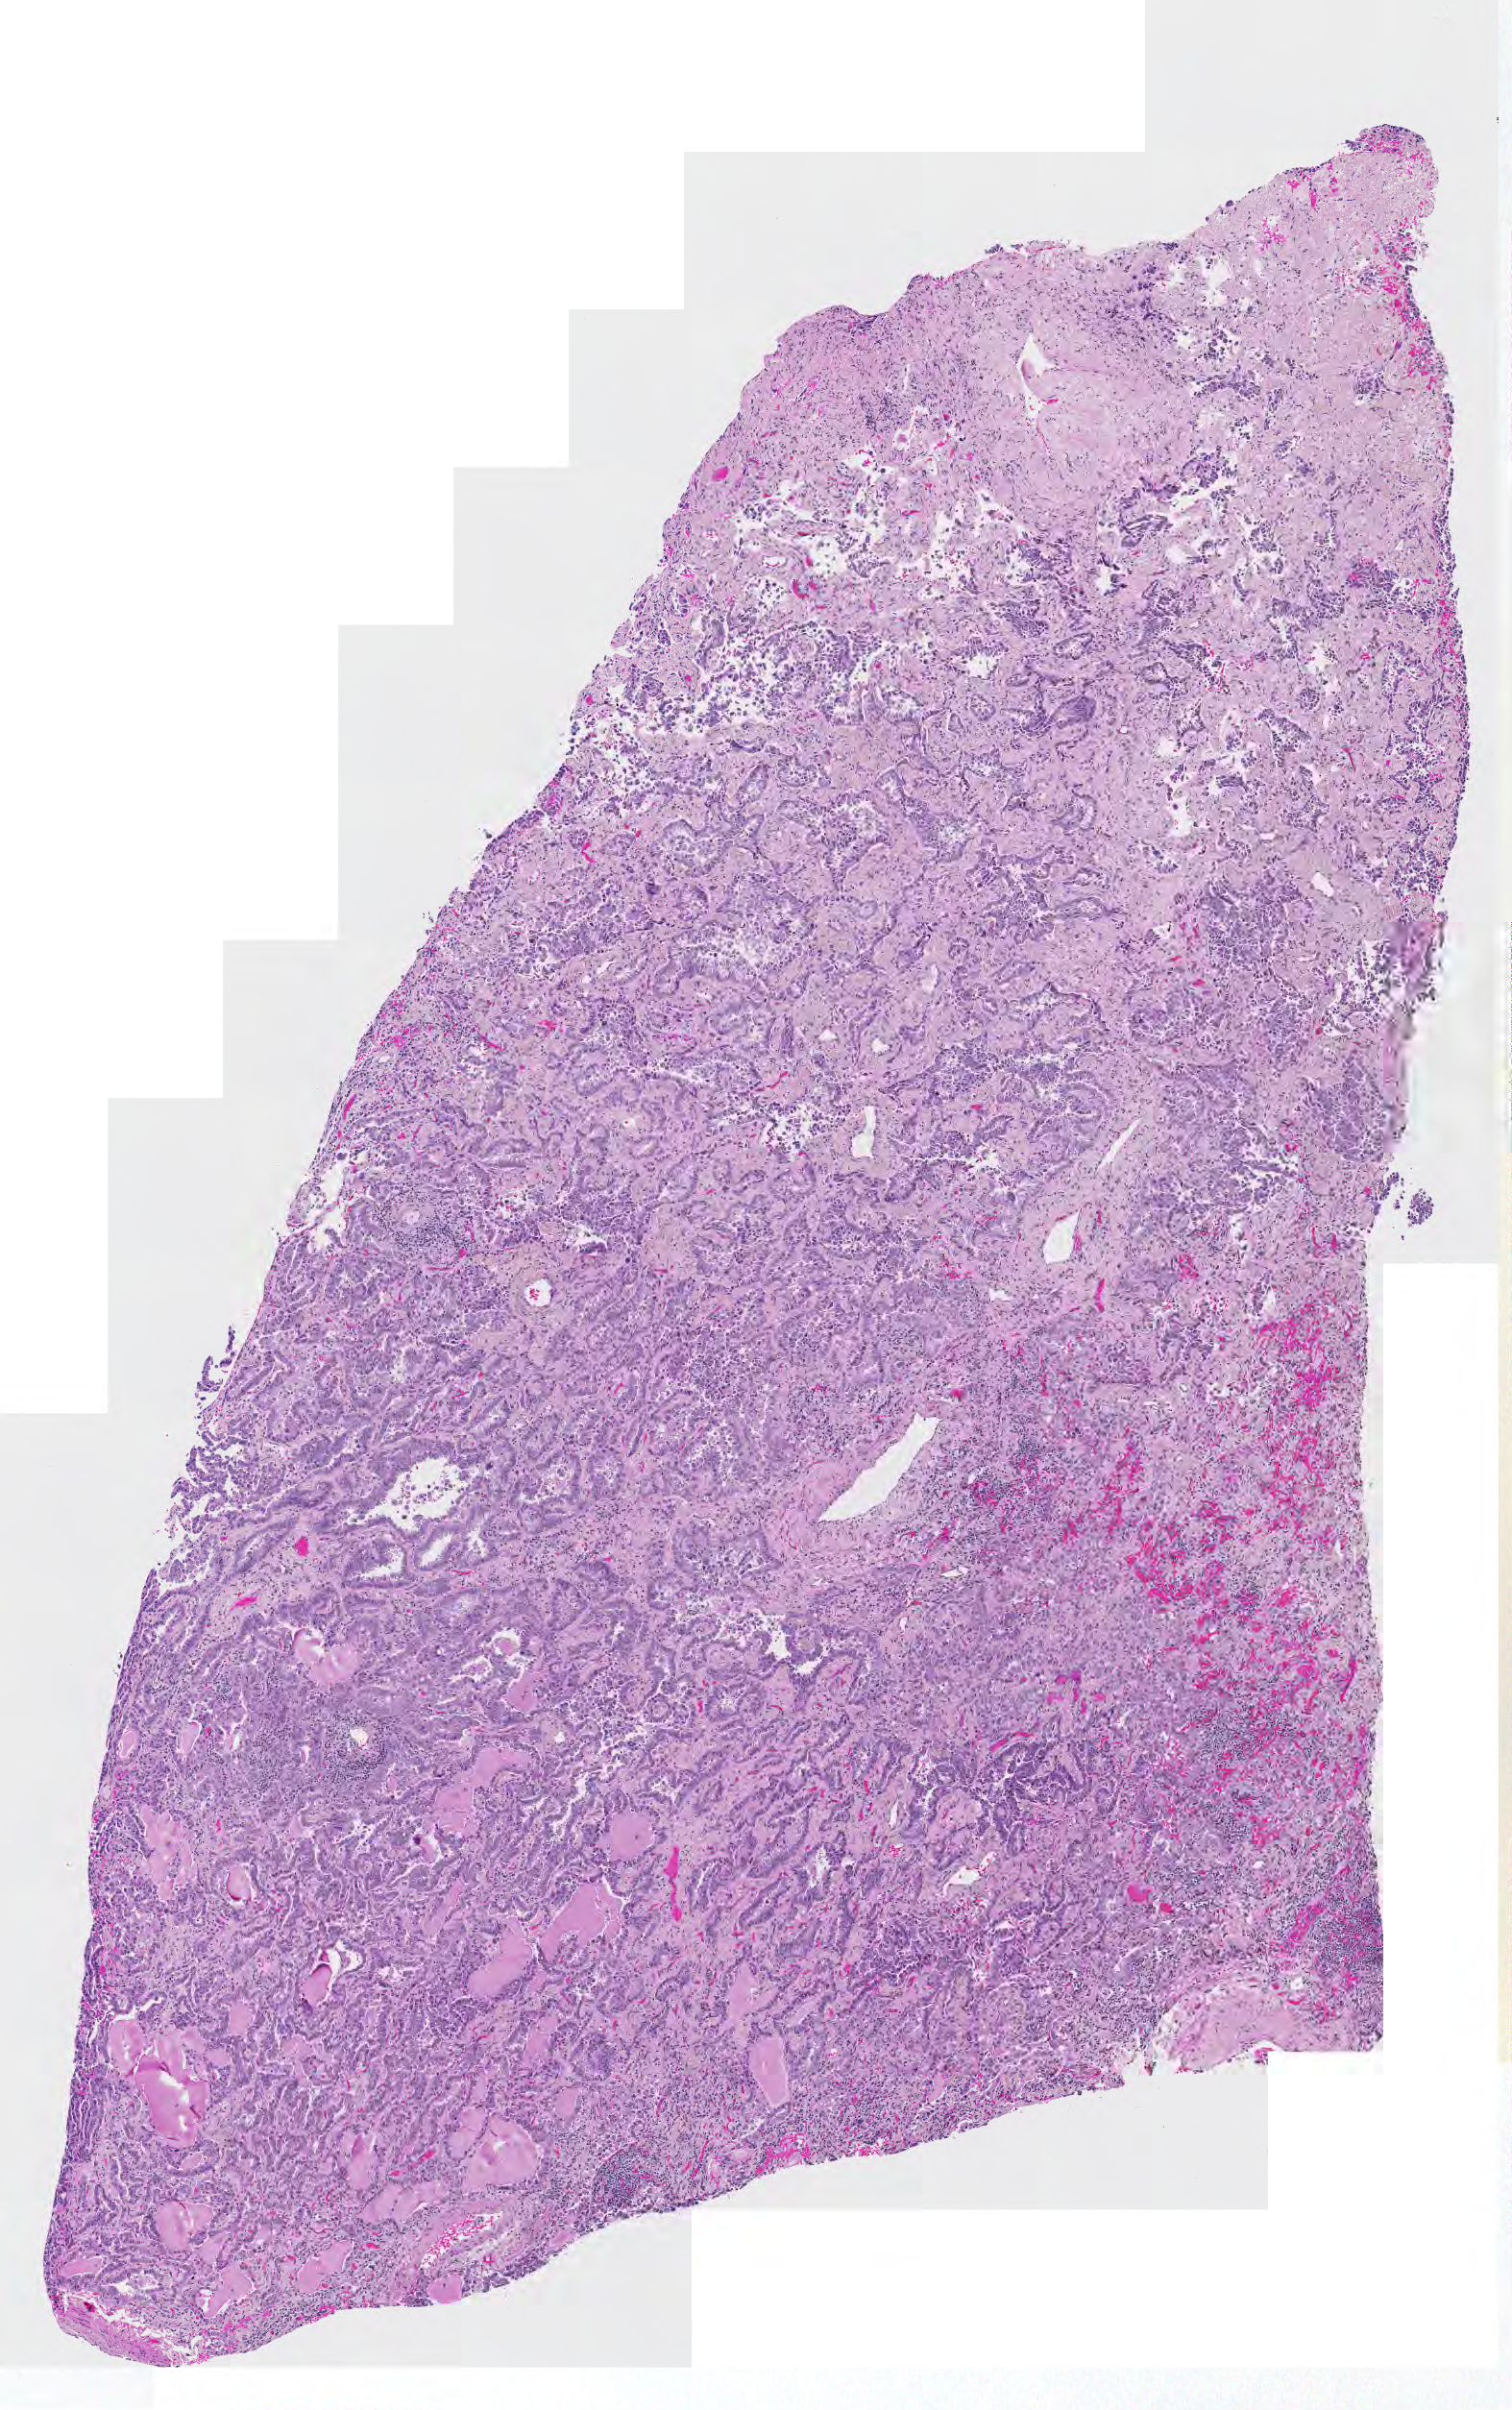
Digitized Hematoxylin and eosin (H&E) stained tissue section (whole slide), shown as a low-resolution overview of the whole scanned area (about 4.1 x 6.5 mm, slide scanned at 20x). Tumour tissue sample, sampled site: lung. Patient: female, age 68 years. Histologic grade: G2 (moderately differentiated). Slide review estimates, as recorded: tumour nuclei 80%, necrosis 3%.
AJCC pathologic stage: IA. Diagnosis: Adenocarcinoma, NOS. Primary tumour site (as recorded): right upper lobe.